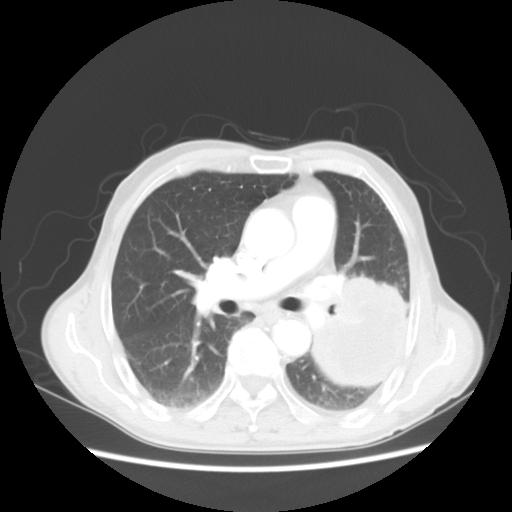
Chest CT, one axial slice. Slice 29 of 51 in the series (ordered by position). Reconstruction kernel STANDARD. Lung window (W 1500 / L -600 HU). 5 mm slice thickness. 512 × 512 image matrix, field of view 360 × 360 mm. Male patient, age 64 years. Case-level facts recorded for this patient, not image findings: clinical TNM (as recorded): T4 N0 M0; histopathological grade: G2-3.
Outlined on this slice (bounding box drawn by a radiologist):
- lung tumour (recorded histology: squamous cell carcinoma): bounding box [x1, y1, x2, y2] px = [317, 273, 408, 390]